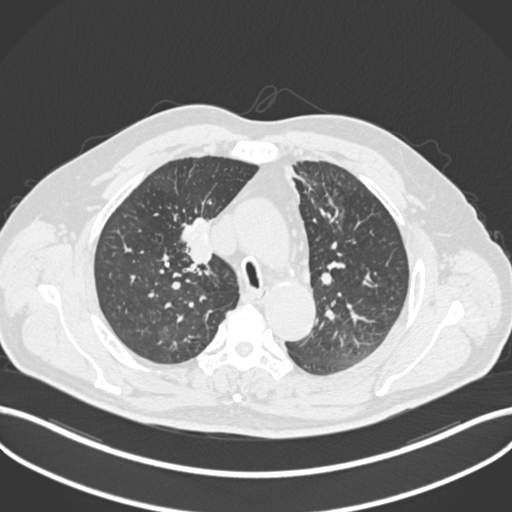
Chest CT, one axial slice; position 140 of 255 along the scan axis; reconstruction kernel B30f; 120 kVp; lung window (W 1500 / L -600 HU); 1 mm slice thickness; 512 × 512 image matrix, field of view 400 × 400 mm. Patient: male, 60 years. Case-level facts recorded for this patient, not image findings: clinical TNM (as recorded): T1b N1 M0.
Outlined on this slice (bounding box drawn by a radiologist):
- lung tumour (recorded histology: squamous cell carcinoma): bounding box [x1, y1, x2, y2] px = [173, 208, 218, 271]